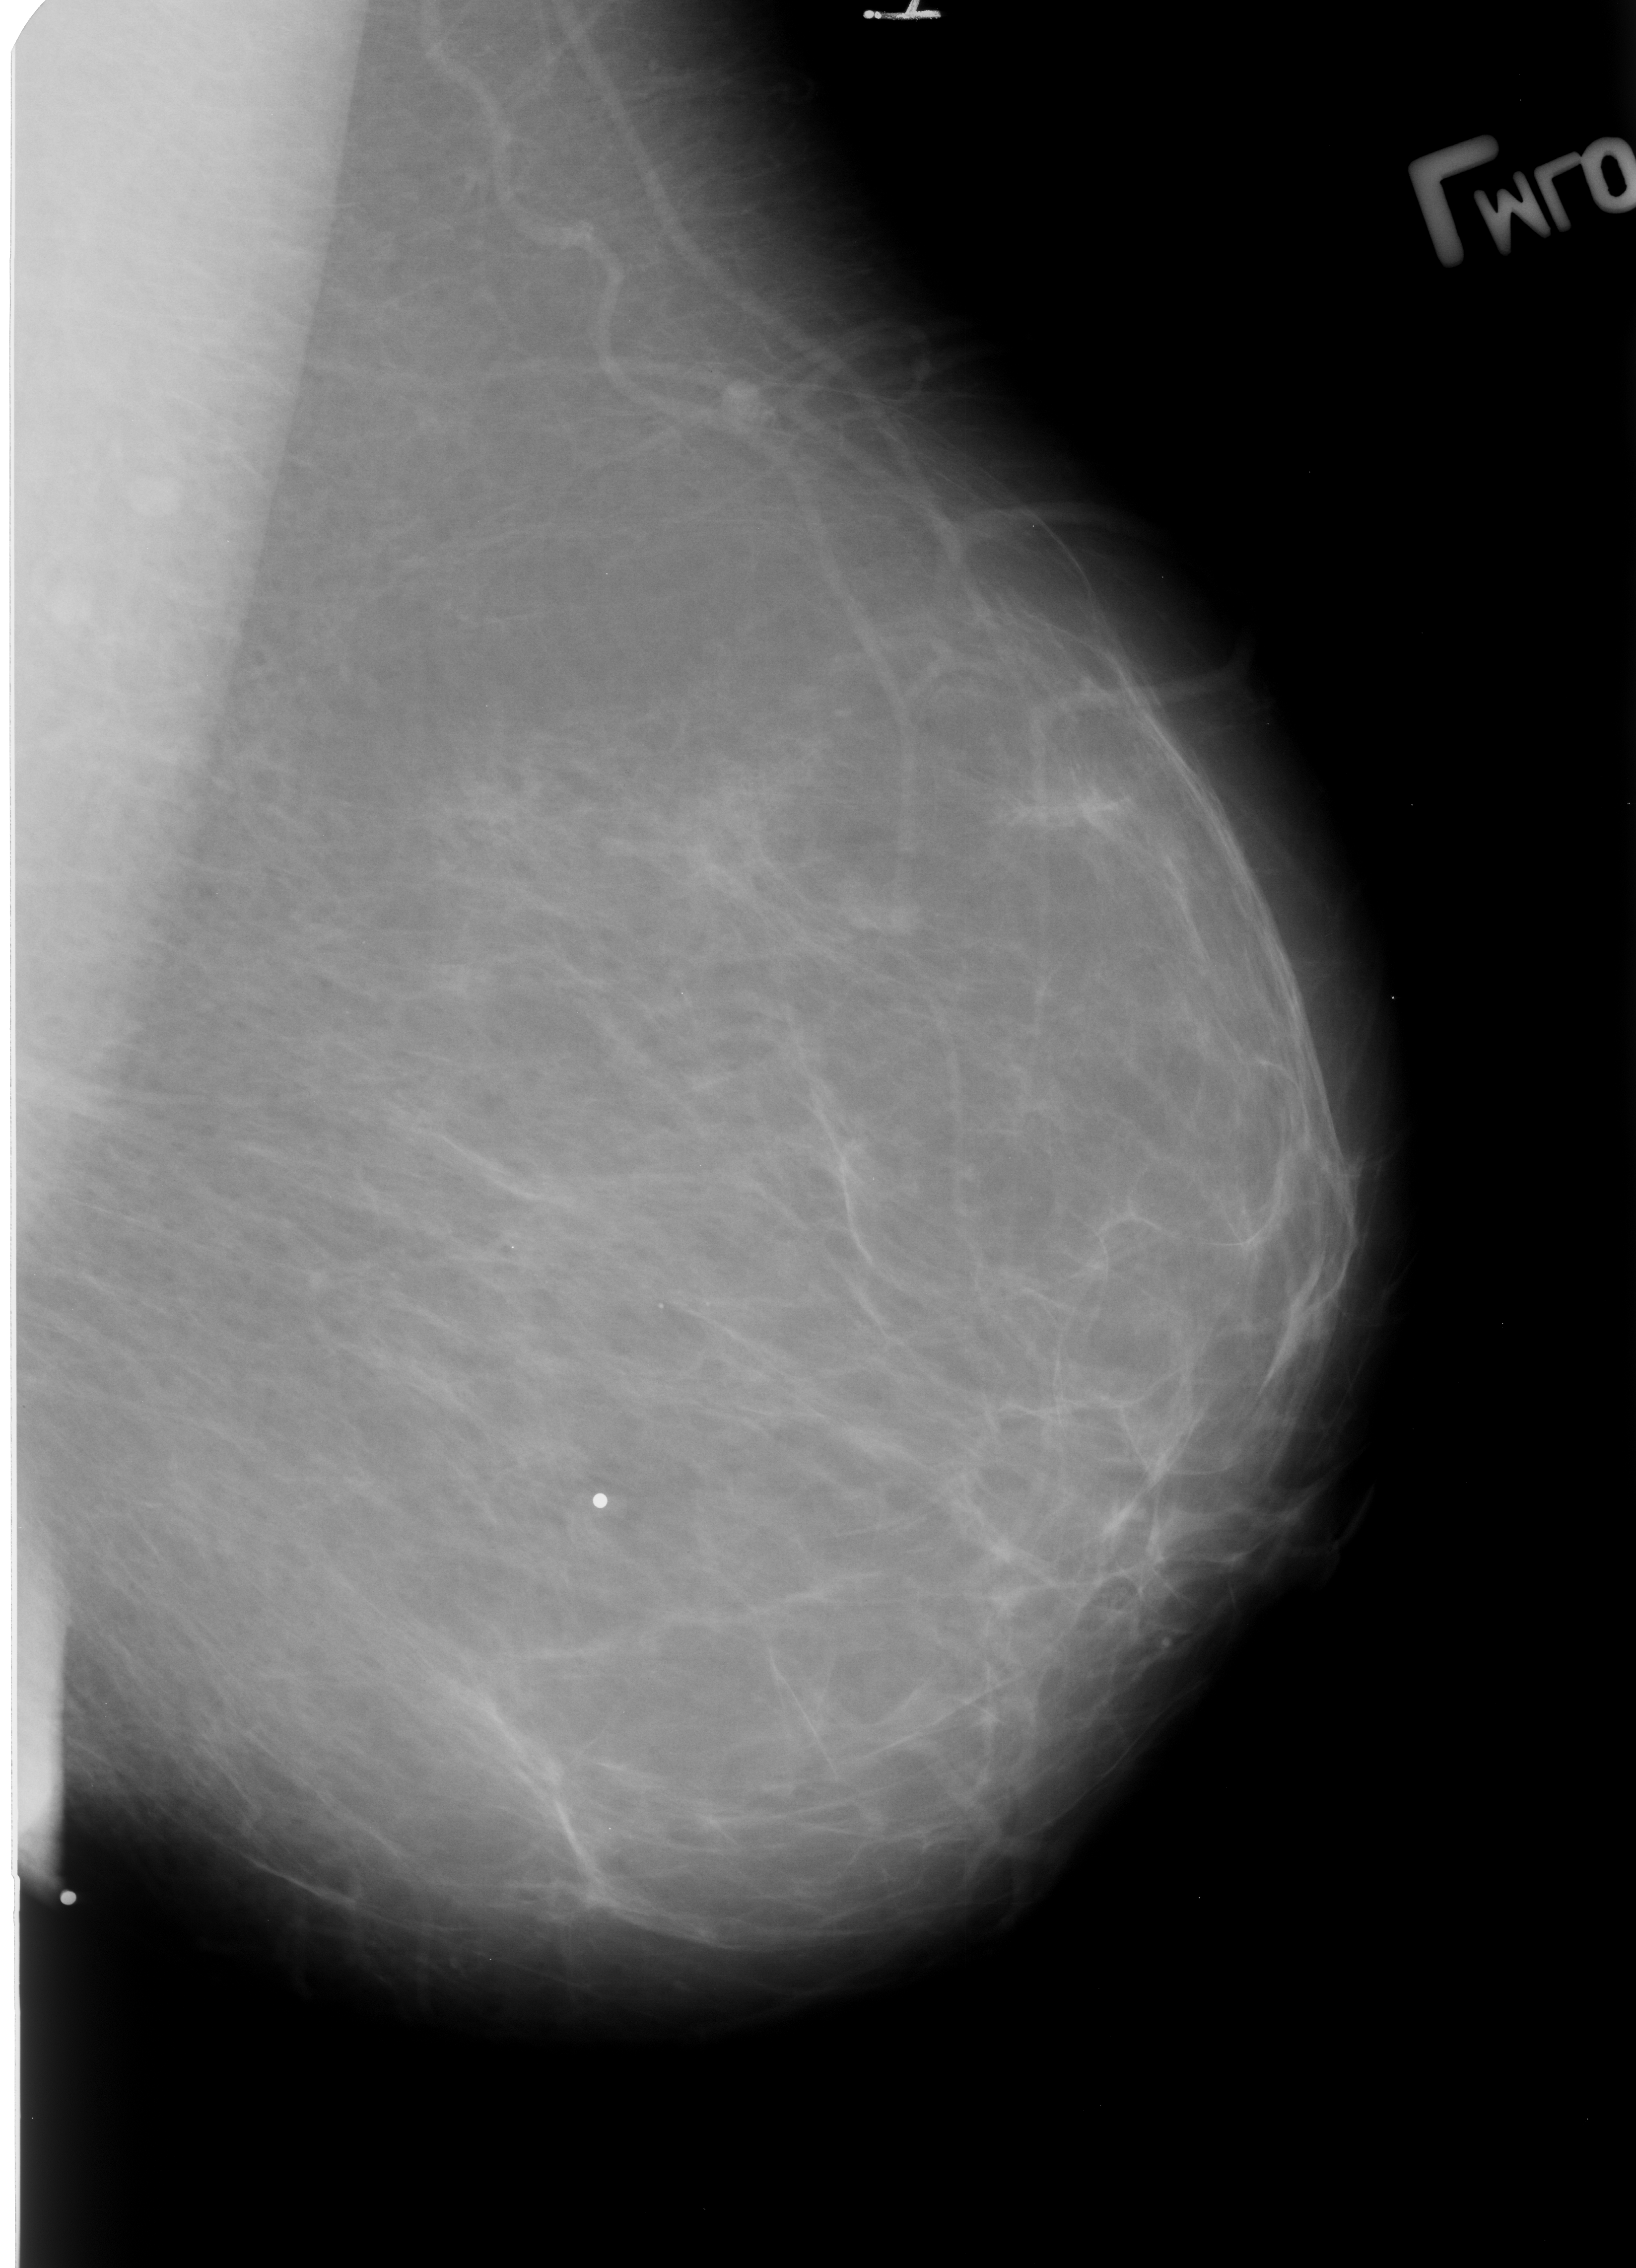
Digitized screen-film mammogram; left breast; MLO view; breast composition: almost entirely fatty (BI-RADS density category 1 of 4); 1636 × 2268 image matrix.
Marked abnormalities (boxes around the expert regions of interest):
- Finding 1 of 2: mass, shape lymph node, margins circumscribed; BI-RADS assessment category 3; outcome (as recorded, no biopsy): benign without callback (not worked up further): bounding box [x1, y1, x2, y2] px = [700, 361, 785, 438]
- Finding 2 of 2: mass, shape lymph node, margins circumscribed; BI-RADS assessment category 3; benign; no additional work-up was recommended (outcome (as recorded, no biopsy): benign without callback): [823, 863, 933, 944]